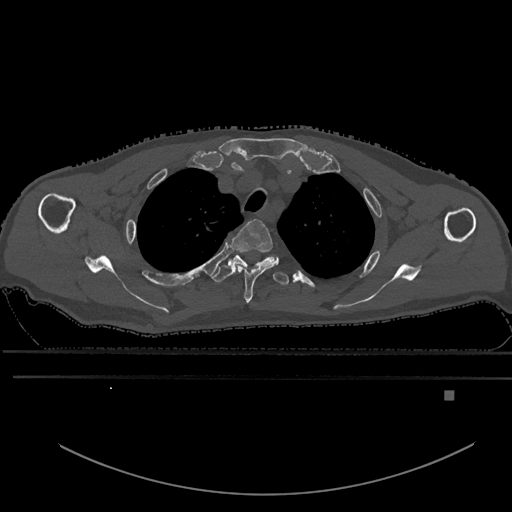
CT including the spine, one axial slice. Slice 477 of 969 in the series (ordered by position). Bone window (W 1800 / L 400 HU). 0.5 mm slice thickness. 512 × 512 image matrix. Male patient, age 82 years. Case-level facts recorded for this patient, not image findings: primary cancer: prostate; vertebrae with lytic lesions (as recorded): T11, T9, T8, T2.
Annotated regions visible in this slice (semi-automatic segmentation, software-assisted and operator-edited):
- T2 vertebra: box from (x=231, y=219) to (x=279, y=303) px
- T3 vertebra: (x=211, y=254)–(x=289, y=286)